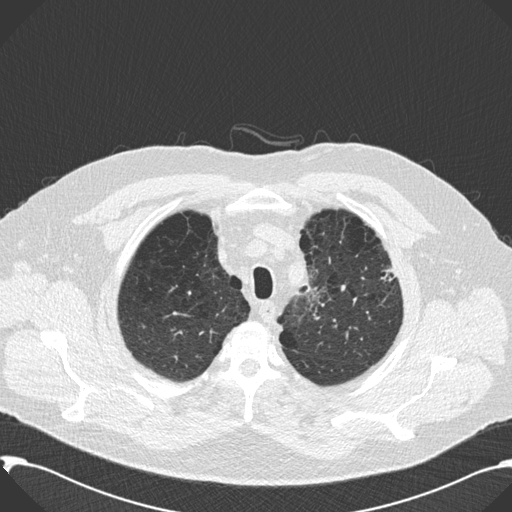
Chest CT (low-dose screening protocol), one axial image. Second screening round (one year after baseline). Lung window (W 1500 / L -600 HU). 512 × 512 image matrix, field of view 380 × 380 mm. Male participant, aged 59 years at enrolment. Current smoker at enrolment.
Lesion marked by an expert reader, bounding box [x1, y1, x2, y2] px = [367, 251, 407, 307]. No non-calcified nodule or mass ≥4 mm was recorded by the screening reader at this exam. Participant outcome: lung cancer diagnosed 518 days after this screen — bronchiolo-alveolar carcinoma, mixed mucinous and non-mucinous, left upper lobe, stage IA (AJCC 6th edition), 20 mm at pathology.